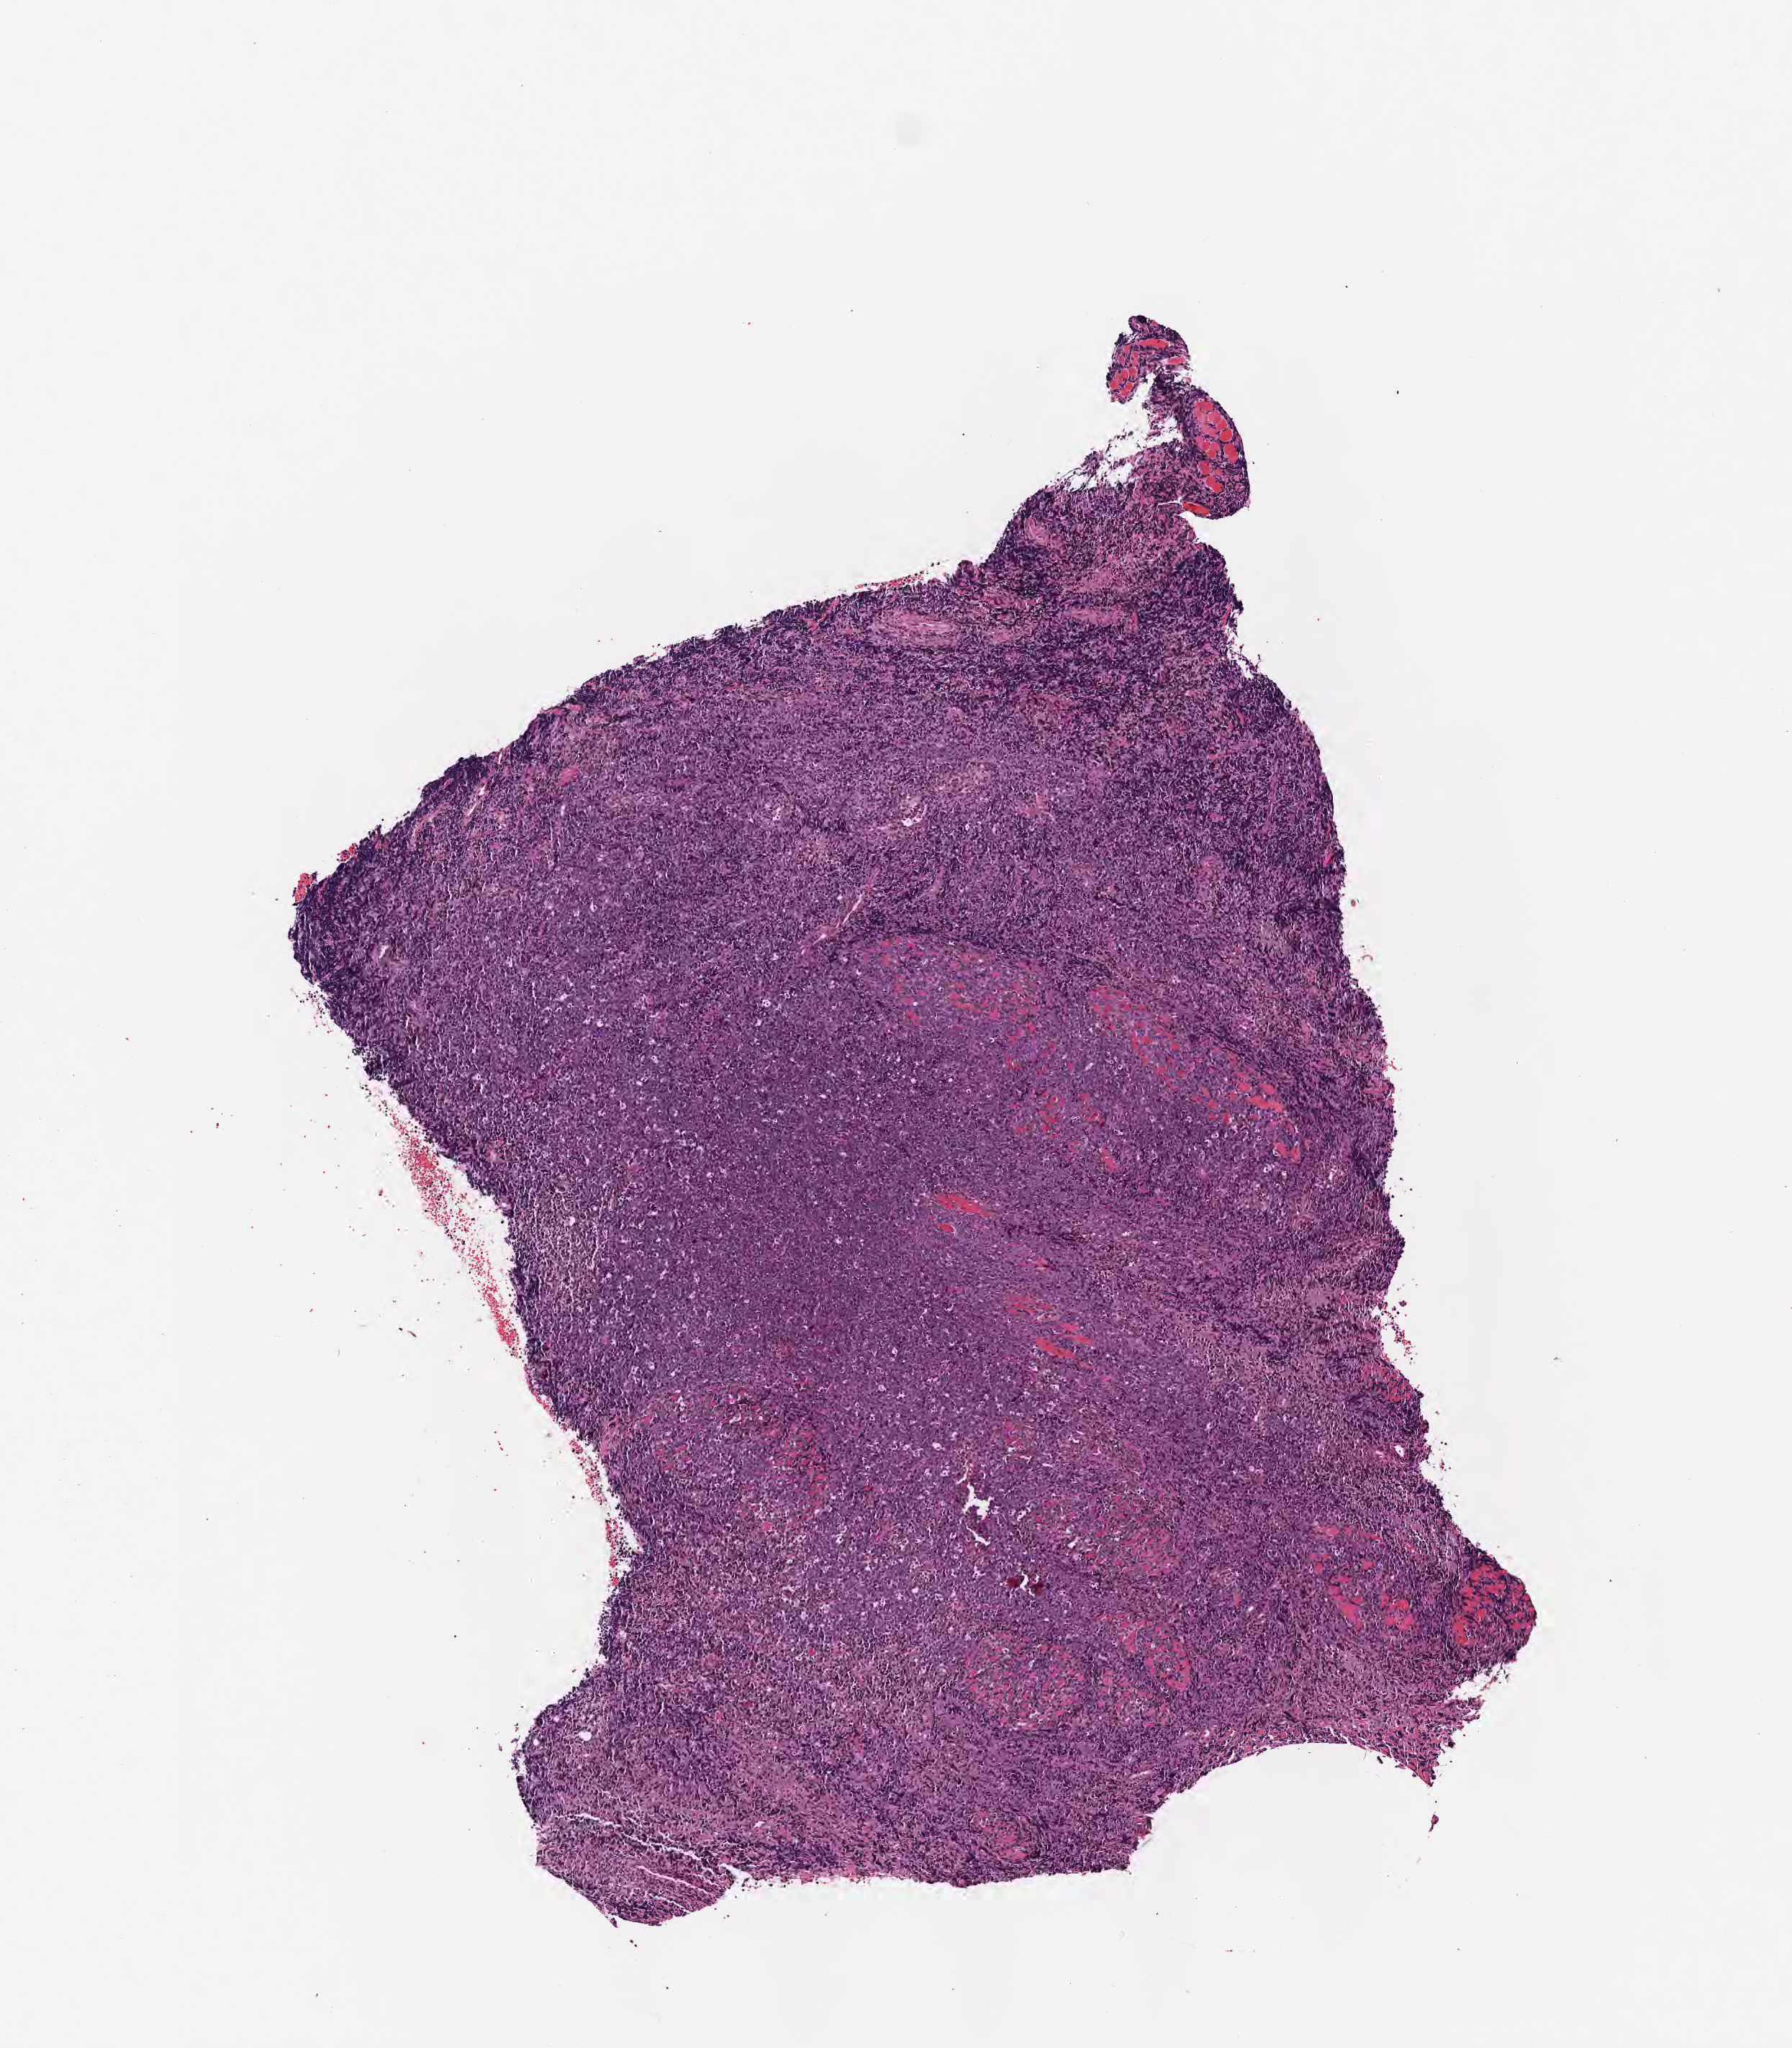
Digitized H&E-stained section — shown as a low-resolution overview of the whole scanned area (about 5.0 x 5.7 mm), FFPE section, specimen: primary tumor, site: cranium. Male patient; age at initial diagnosis 5 years. Pathologist review of this section (percent, as recorded): tumor cells 90%, tumor nuclei 90%, stromal cells 10%, necrosis 0%, normal cells 0%. Inflammatory infiltration, as recorded: lymphocyte infiltration 20%, monocyte infiltration 30%, neutrophil infiltration 10%.
* section: bottom of the tissue portion
* histologic diagnosis: Burkitt lymphoma, NOS
* Ann Arbor stage (patient): Stage IV